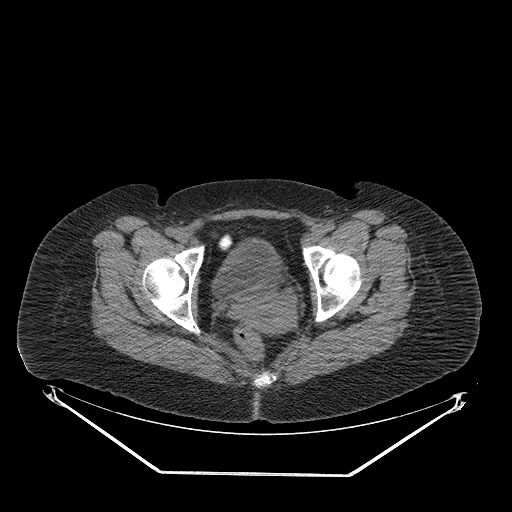
CT of an extremity soft-tissue mass (from a PET/CT study), one axial slice; slice 62 of 267 in the series (ordered by position); soft-tissue window (W 400 / L 40 HU); 3.75 mm slice thickness; 512 × 512 image matrix, field of view 500 × 500 mm. Female patient. Case-level facts recorded for this patient, not image findings: histological type: myxofibrosarcoma; grade: intermediate; site of the primary tumour: left thigh.
Outlined on this slice (expert contour drawn on MRI and transferred to this co-registered scan by the dataset authors):
- gross tumour volume including surrounding oedema: box from (x=308, y=231) to (x=328, y=250) px